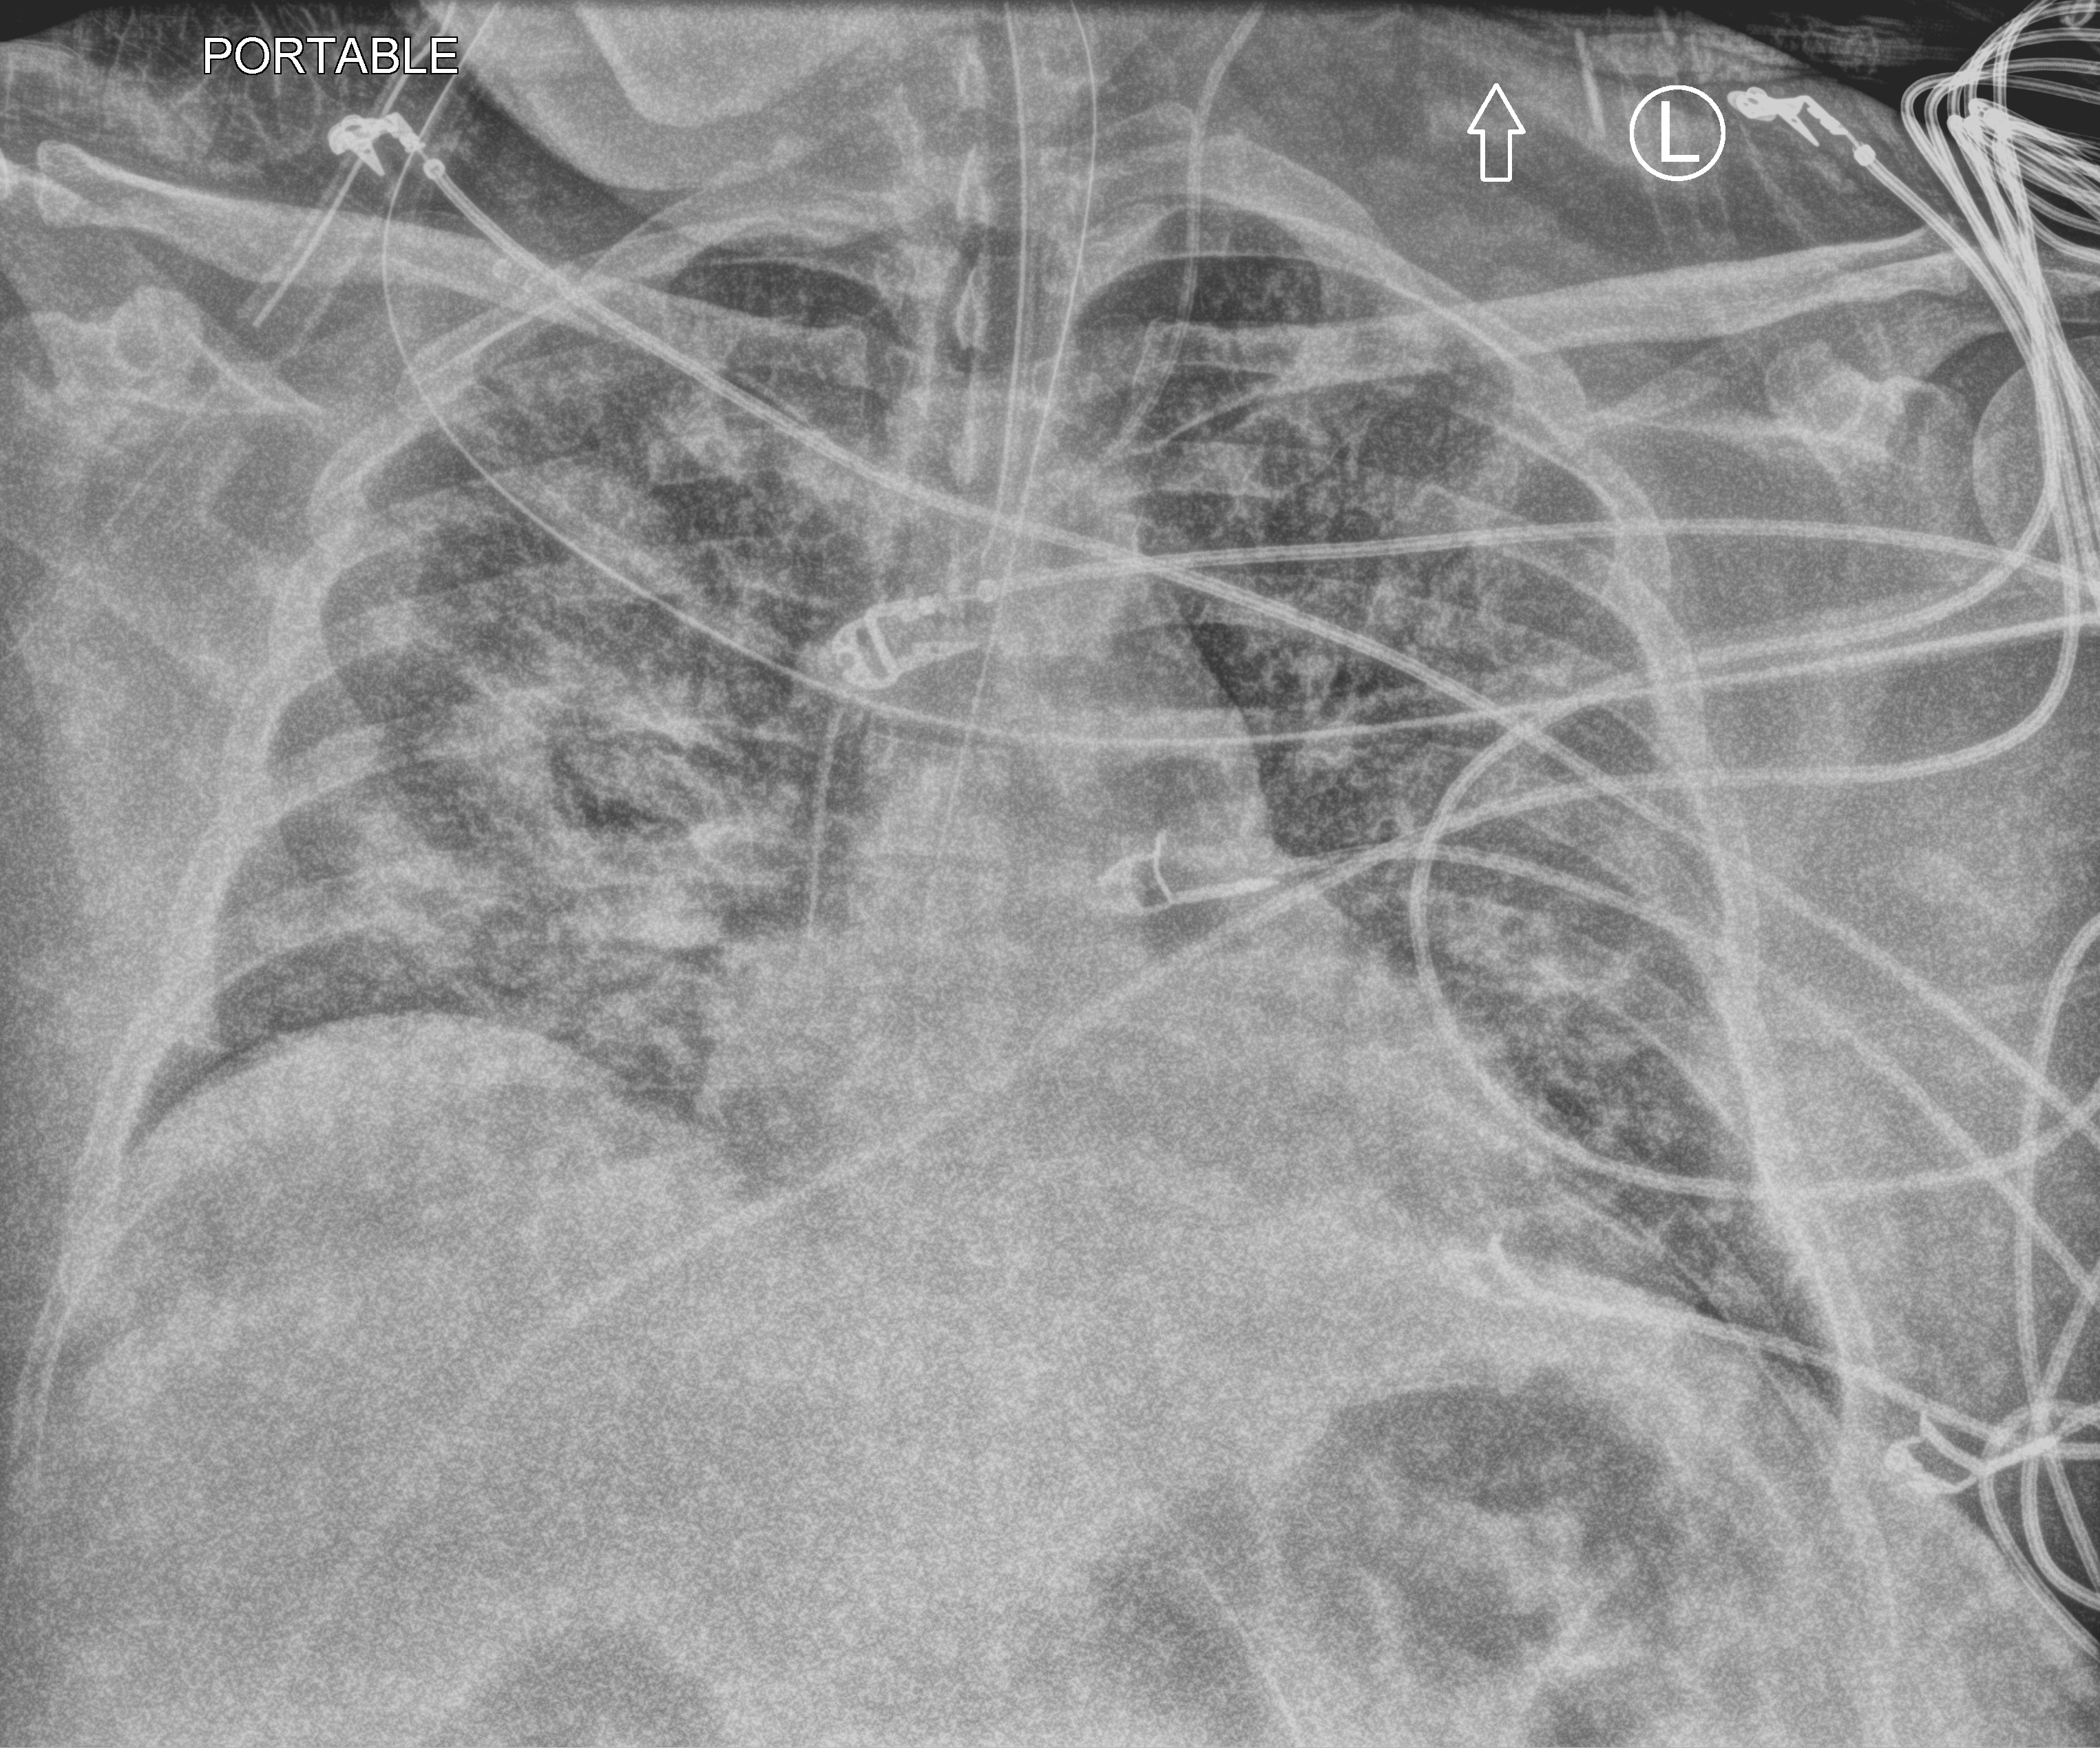
Portable chest radiograph; anteroposterior (AP) projection. Patient hospitalised with COVID-19, aged 18–59 years.
From the hospital-stay record, not from the radiograph (when in the stay this image was taken is not recorded): chronic kidney disease (admission record): no; admitted to intensive care during this hospital stay: yes; length of hospital stay: 16 days.